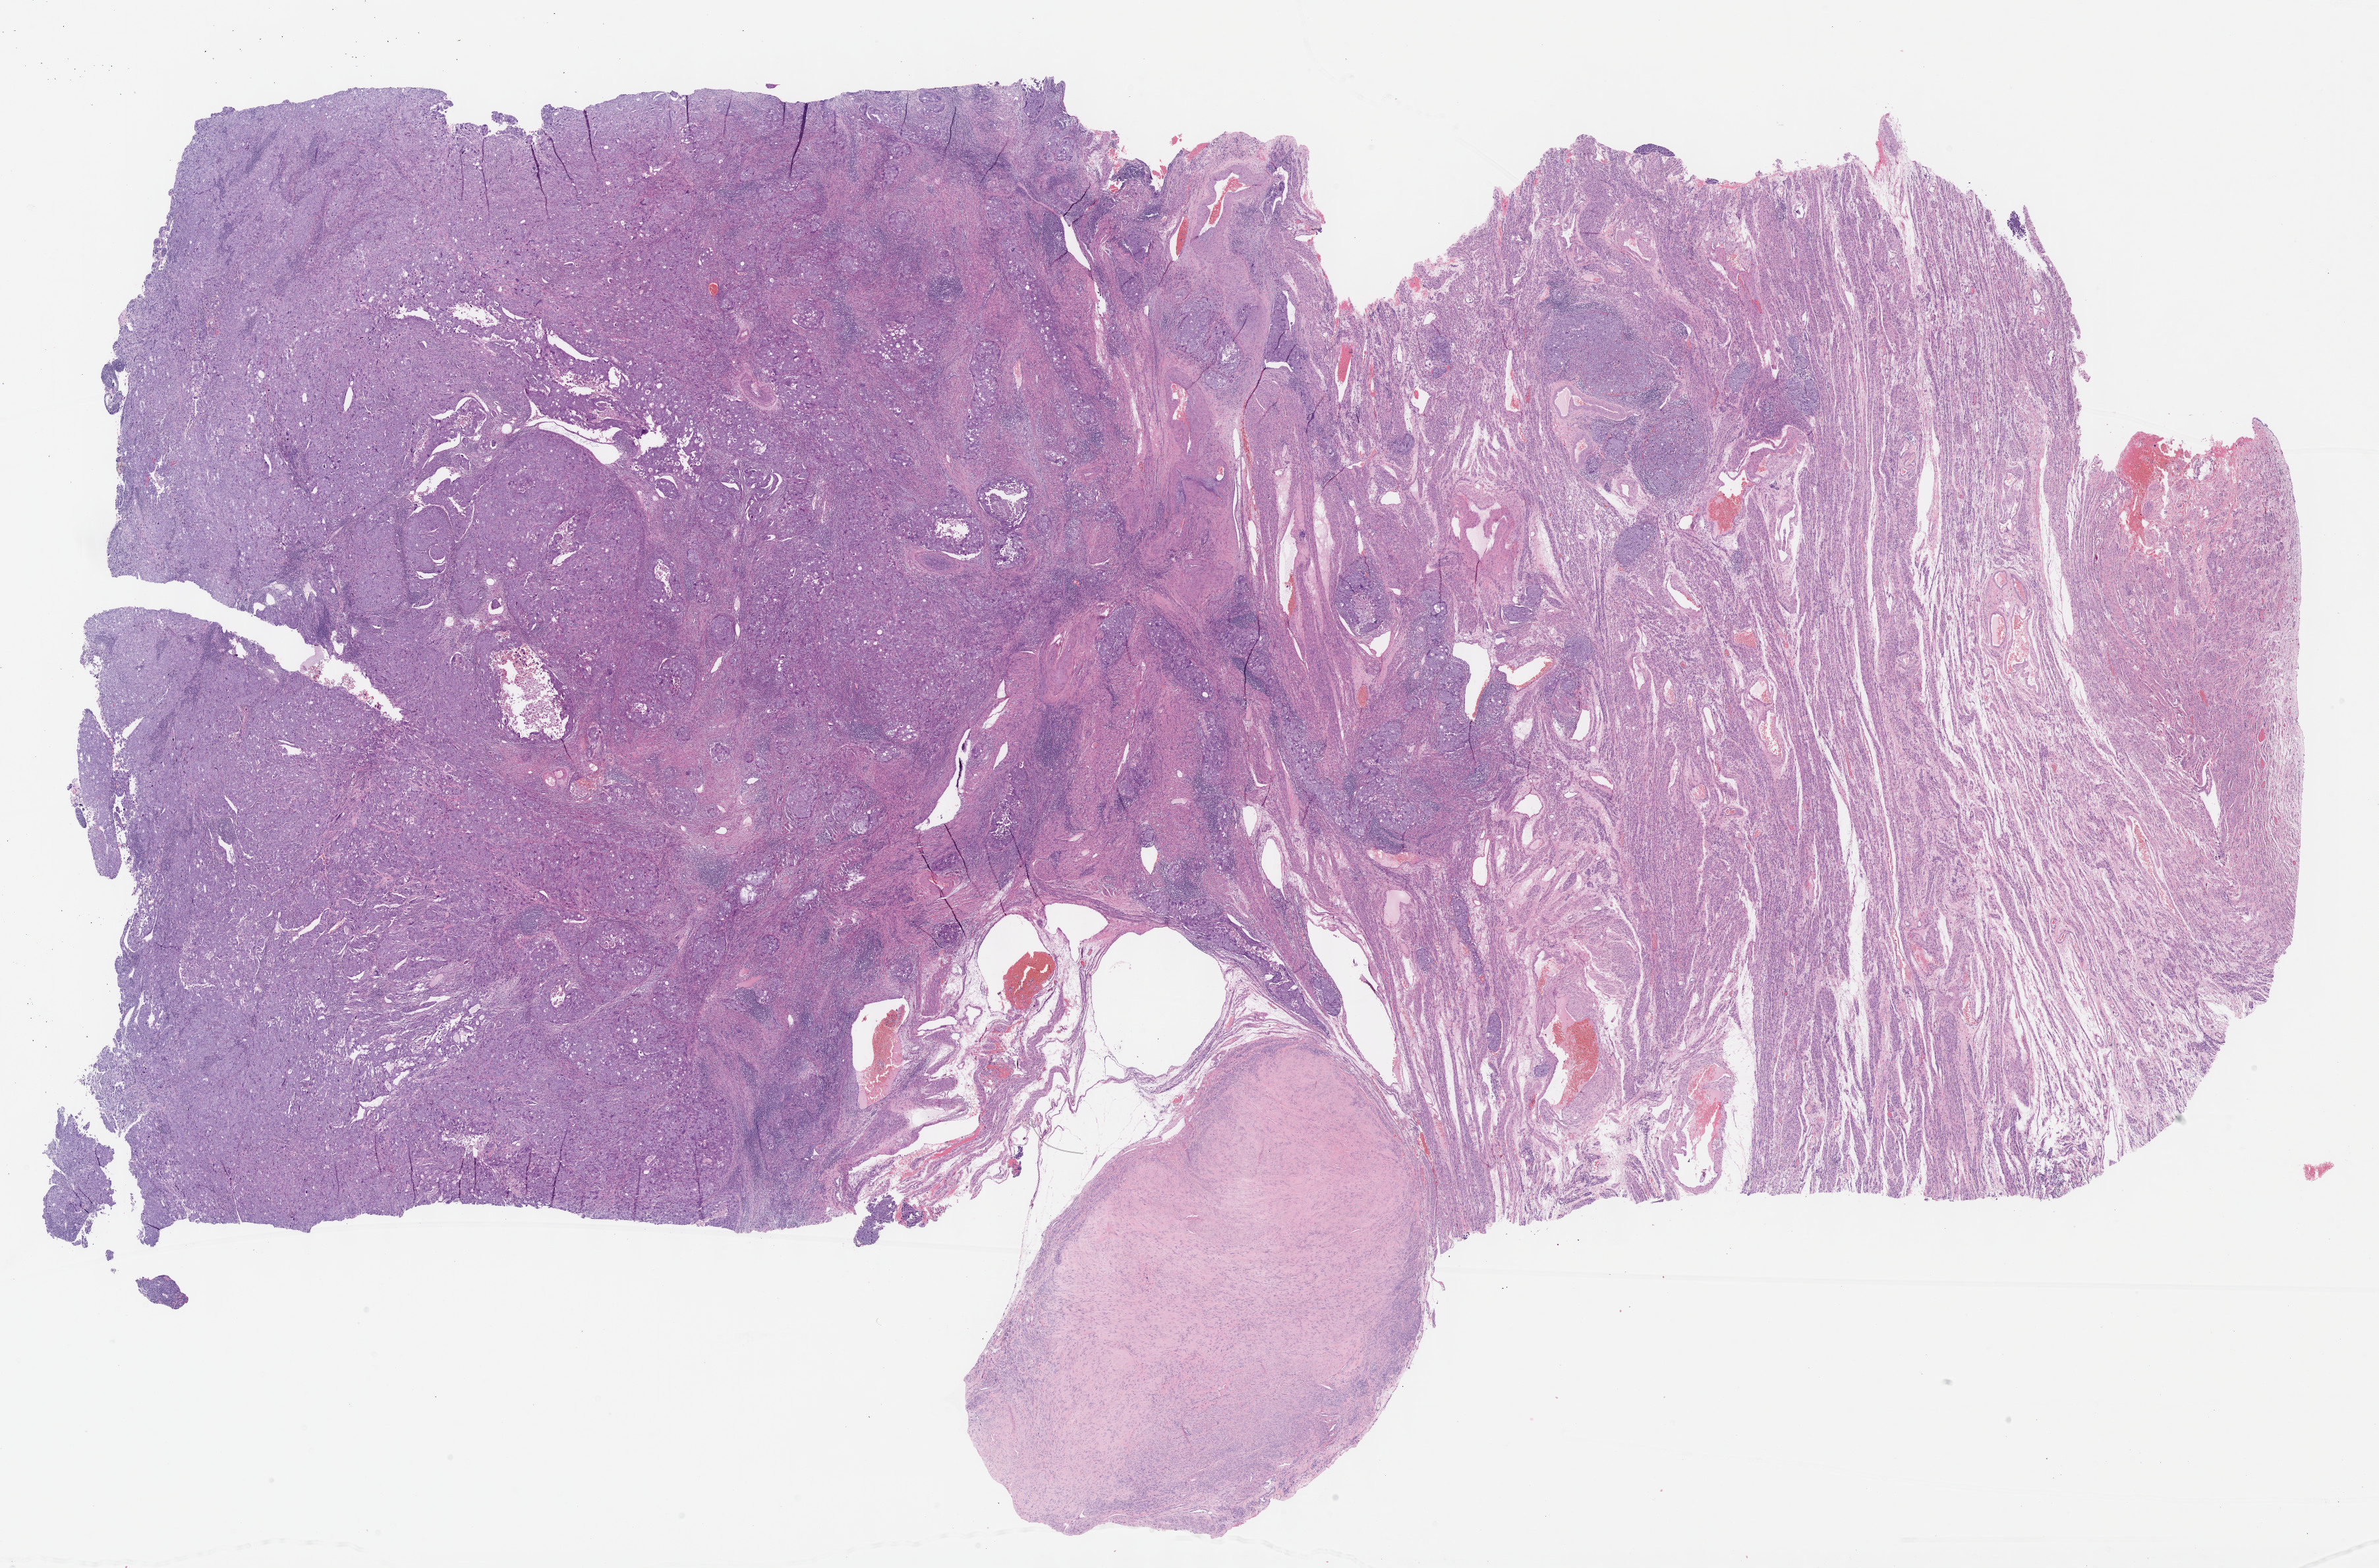
Digitized H&E tissue section (whole slide) — whole scanned area (about 29.2 x 19.2 mm) shown as a low-resolution overview; formalin-fixed paraffin-embedded (FFPE) diagnostic section; sample: primary tumour, uterus. Female, age 61 years at initial diagnosis. Histologic grade: G3 (poorly differentiated).
Lymph nodes positive (case pathology): 0 of 2 examined. FIGO stage: IIIC1. Histologic diagnosis: Serous cystadenocarcinoma, NOS (endometrium).